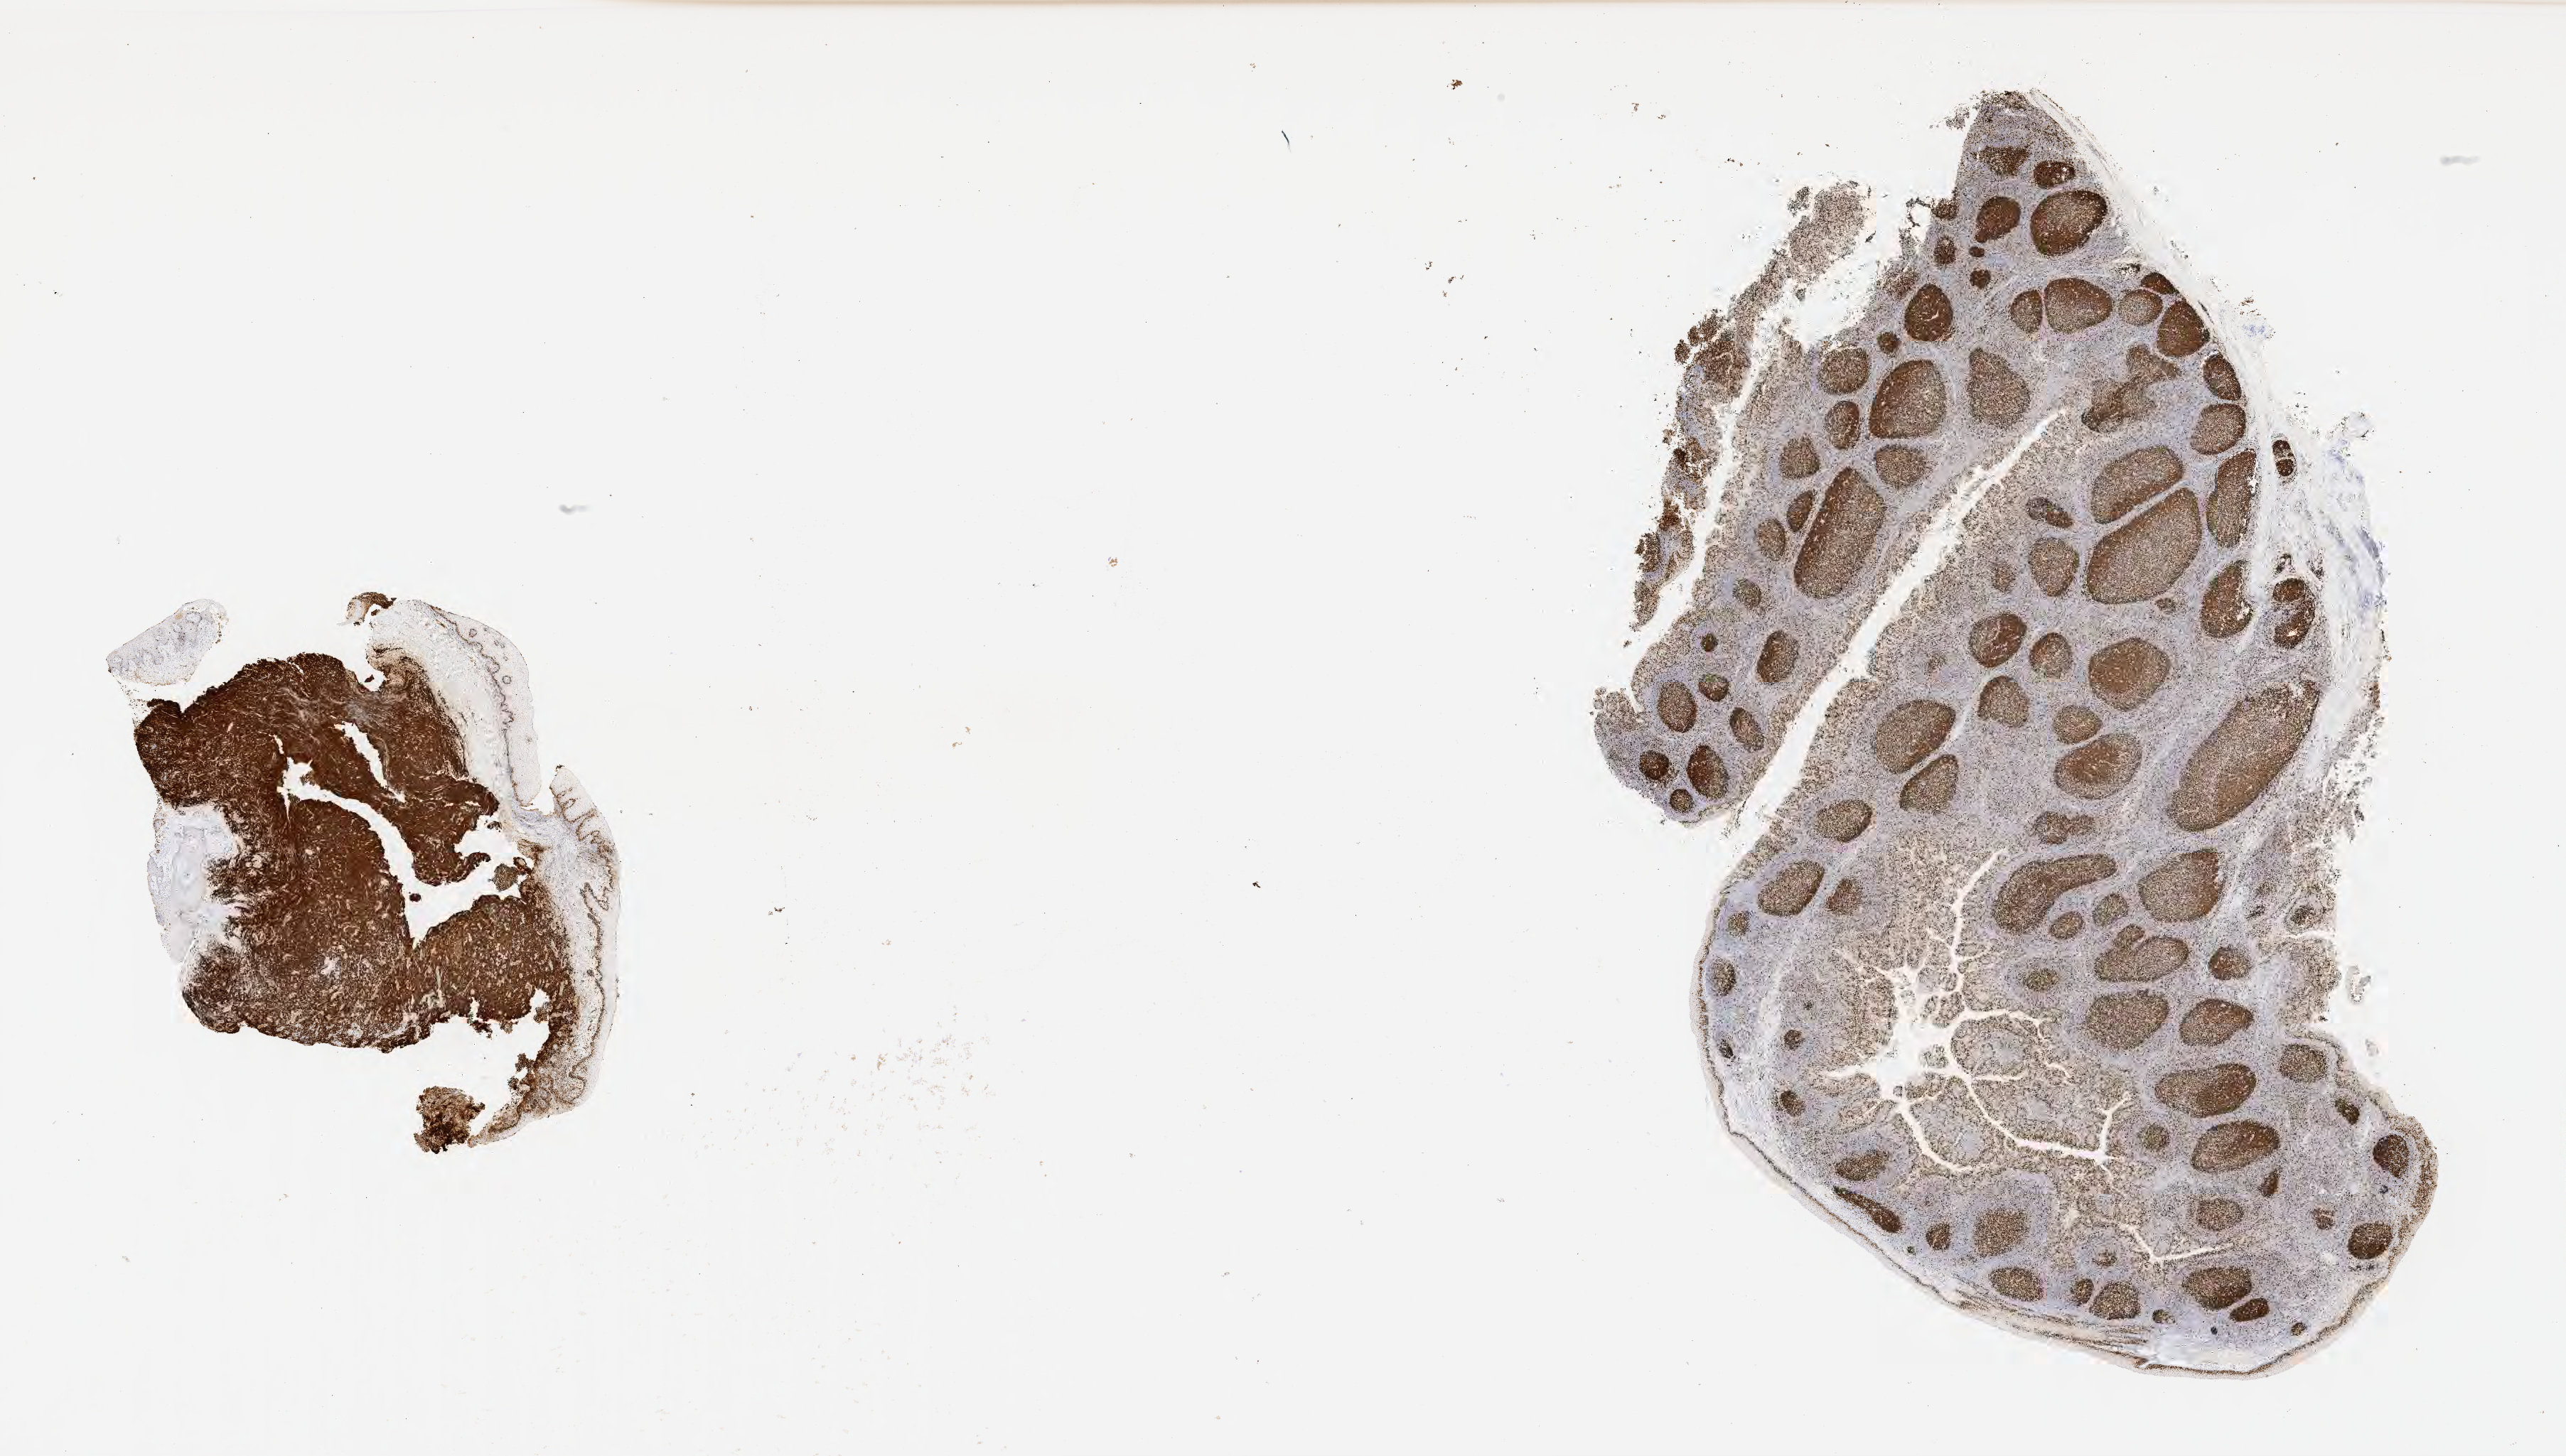
Whole-slide image, immunohistochemical stain for Ki-67 — shown as a low-resolution overview of the whole scanned area (about 29.2 x 16.6 mm), tumor tissue, site: mandible. Female patient; age at initial diagnosis 7 years.
Diagnosis: Burkitt lymphoma, NOS.